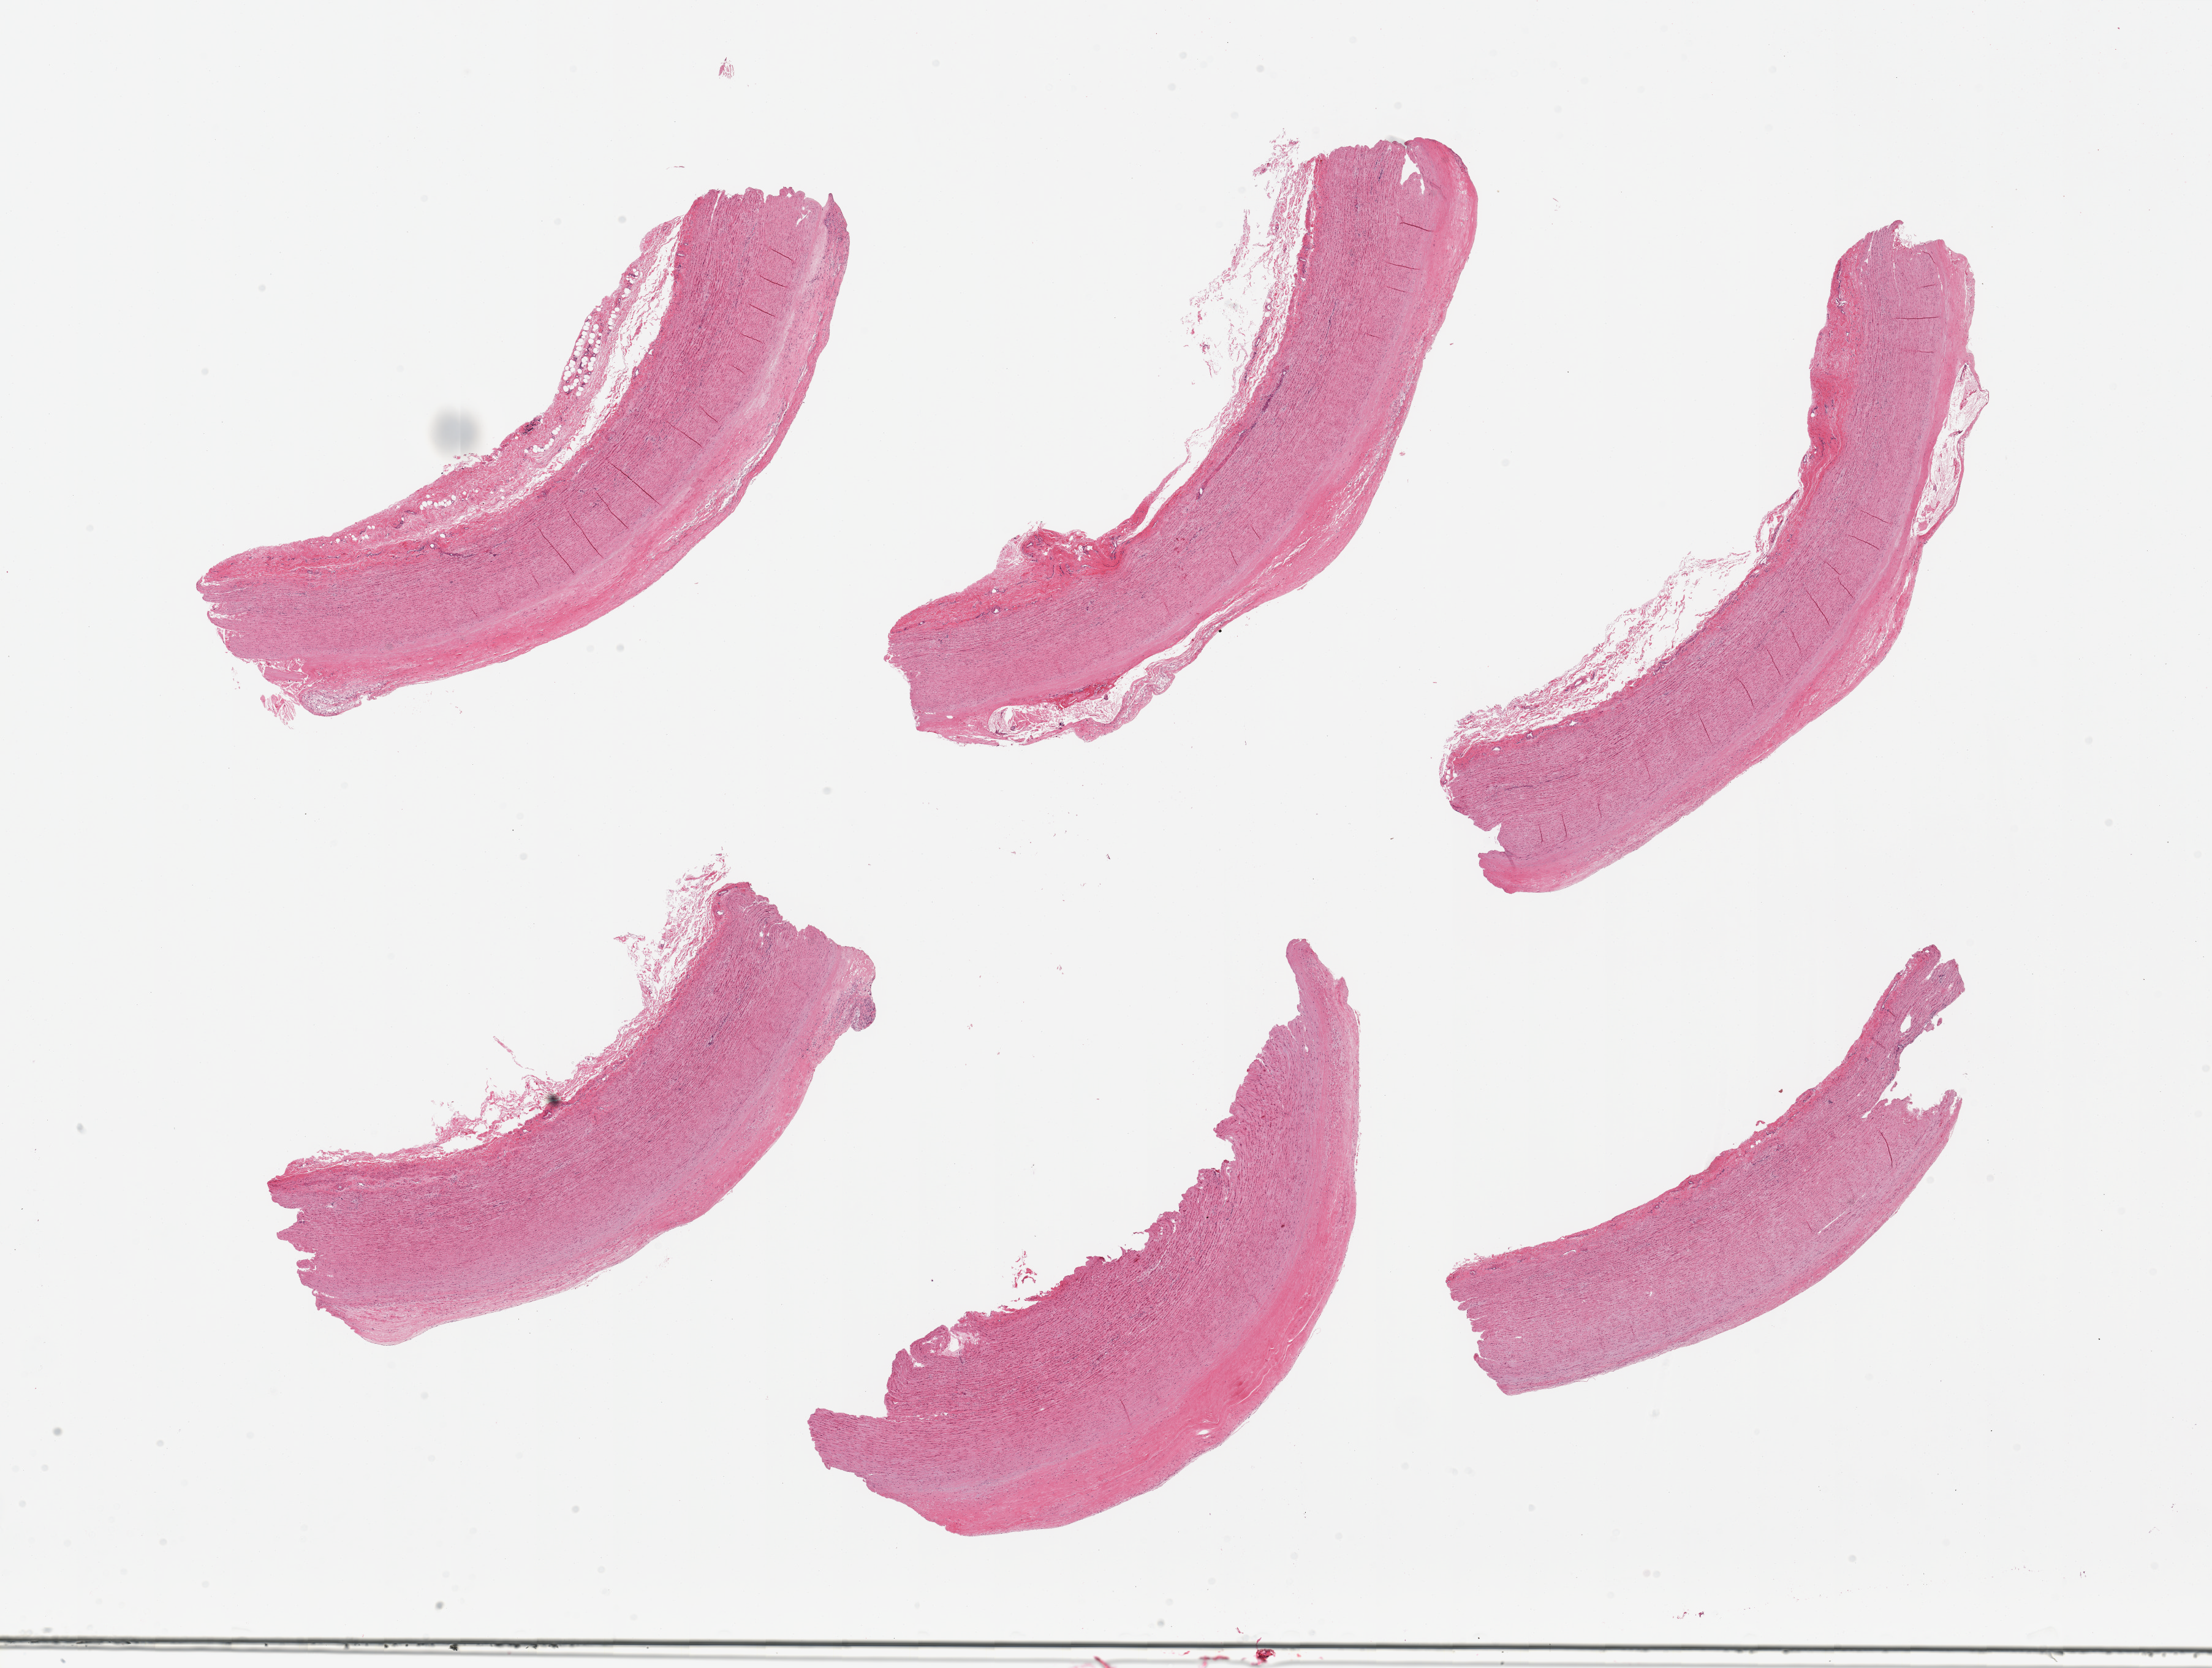
Whole-slide image, hematoxylin and eosin (H&E) stain, low-resolution overview of the scanned area, about 28.5 x 21.5 mm (acquisition: 20x scan). PAXgene-fixed, paraffin-embedded tissue. Target tissue: aorta. Donor tissue sample. Donor: male.
Review note (as recorded): 6 pieces; atherosclerosis and atheroma with cholesterol clefts.